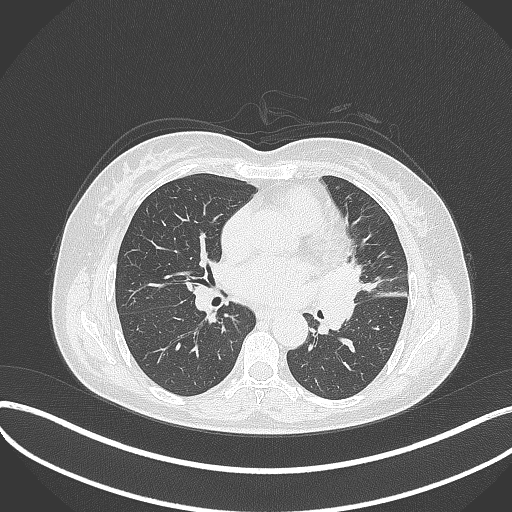
Chest CT, one axial slice; position 178 of 373 along the scan axis; reconstruction kernel B70f; lung window (W 1500 / L -600 HU); 512 × 512 image matrix. Female patient, age 54 years. From the clinical record (not read from this slice): clinical TNM (as recorded): T2a N1 M0.
Annotated regions visible in this slice (bounding box drawn by a radiologist):
- lung tumour (recorded histology: small cell carcinoma): box from (x=315, y=258) to (x=368, y=336) px